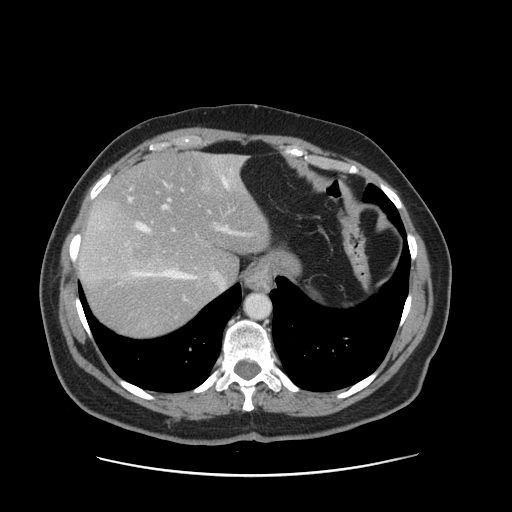
Contrast-enhanced abdominal CT, one axial slice; slice 120 of 161 in the series (ordered by position); intravenous contrast given; soft-tissue window (W 400 / L 40 HU); 2.5 mm slice thickness; 512 × 512 image matrix, field of view 398 × 398 mm. Female patient, age 62 years. From the clinical record (not read from this slice): diagnosis: colorectal cancer liver metastases, imaged before liver resection; multiple liver metastases: no; largest metastasis: 2.5 cm; disease in both lobes: no.
Annotated regions visible in this slice (outlined manually by an expert reader):
- hepatic veins: bounding box [x1, y1, x2, y2] px = [129, 157, 244, 289]
- liver: [79, 154, 270, 338]
- planned liver remnant (the part of the liver to remain after resection): [95, 153, 270, 281]
- portal vein (with intrahepatic branches): [161, 187, 246, 235]